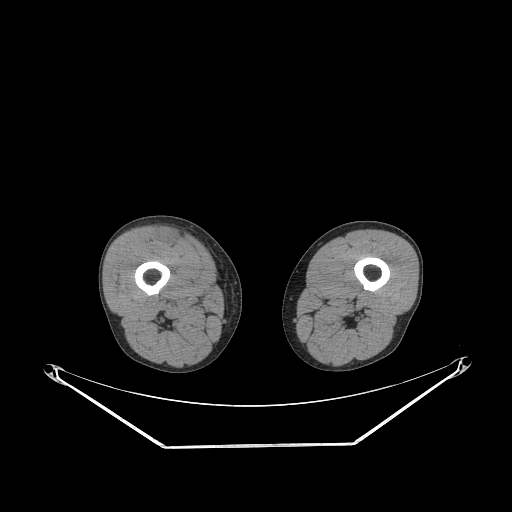
CT of an extremity soft-tissue mass (from a PET/CT study), one axial slice. Slice 230 of 311 in the series (ordered by position). Reconstruction kernel STANDARD. 140 kVp. Soft-tissue window (W 400 / L 40 HU). 3.75 mm slice thickness. 512 × 512 image matrix, field of view 500 × 500 mm. Male patient. From the clinical record (not read from this slice): histological type: pleiomorphic leiomyosarcoma; grade: intermediate; site of the primary tumour: right thigh.
Outlined on this slice (expert contour drawn on MRI and transferred to this co-registered scan by the dataset authors):
- gross tumour volume including surrounding oedema: box from (x=158, y=228) to (x=182, y=247) px